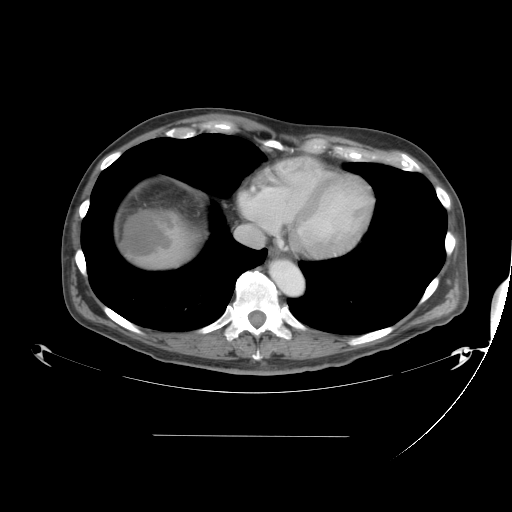
Contrast-enhanced abdominal CT, one axial slice; slice 41 of 48 in the series (ordered by position); reconstruction kernel STANDARD; 120 kVp; intravenous contrast given; soft-tissue window (W 400 / L 40 HU); 5 mm slice thickness; 512 × 512 image matrix. Male patient, age 65 years. Case-level facts recorded for this patient, not image findings: diagnosis: colorectal cancer liver metastases, imaged before liver resection; multiple liver metastases: yes; largest metastasis: 11 cm; disease in both lobes: yes.
Structures marked on this image (expert manual segmentation):
- liver: box from (x=120, y=209) to (x=202, y=274) px
- liver metastasis: (x=119, y=210)–(x=172, y=256)